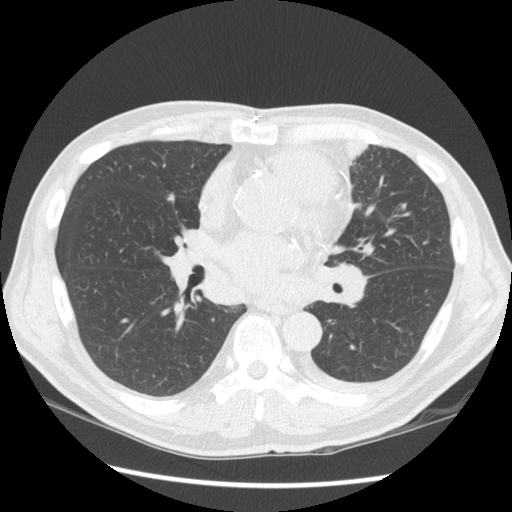
Low-dose screening chest CT, one axial slice; position 73 of 136 along the scan axis; lung window (W 1500 / L -600 HU); 512 × 512 image matrix, field of view 360 × 360 mm.
Structures marked on this image (manually delineated by an expert):
- lesion 1 (tumor, upper lobe of left lung): bounding box <330,140,368,167> (left, top, right, bottom; pixels)